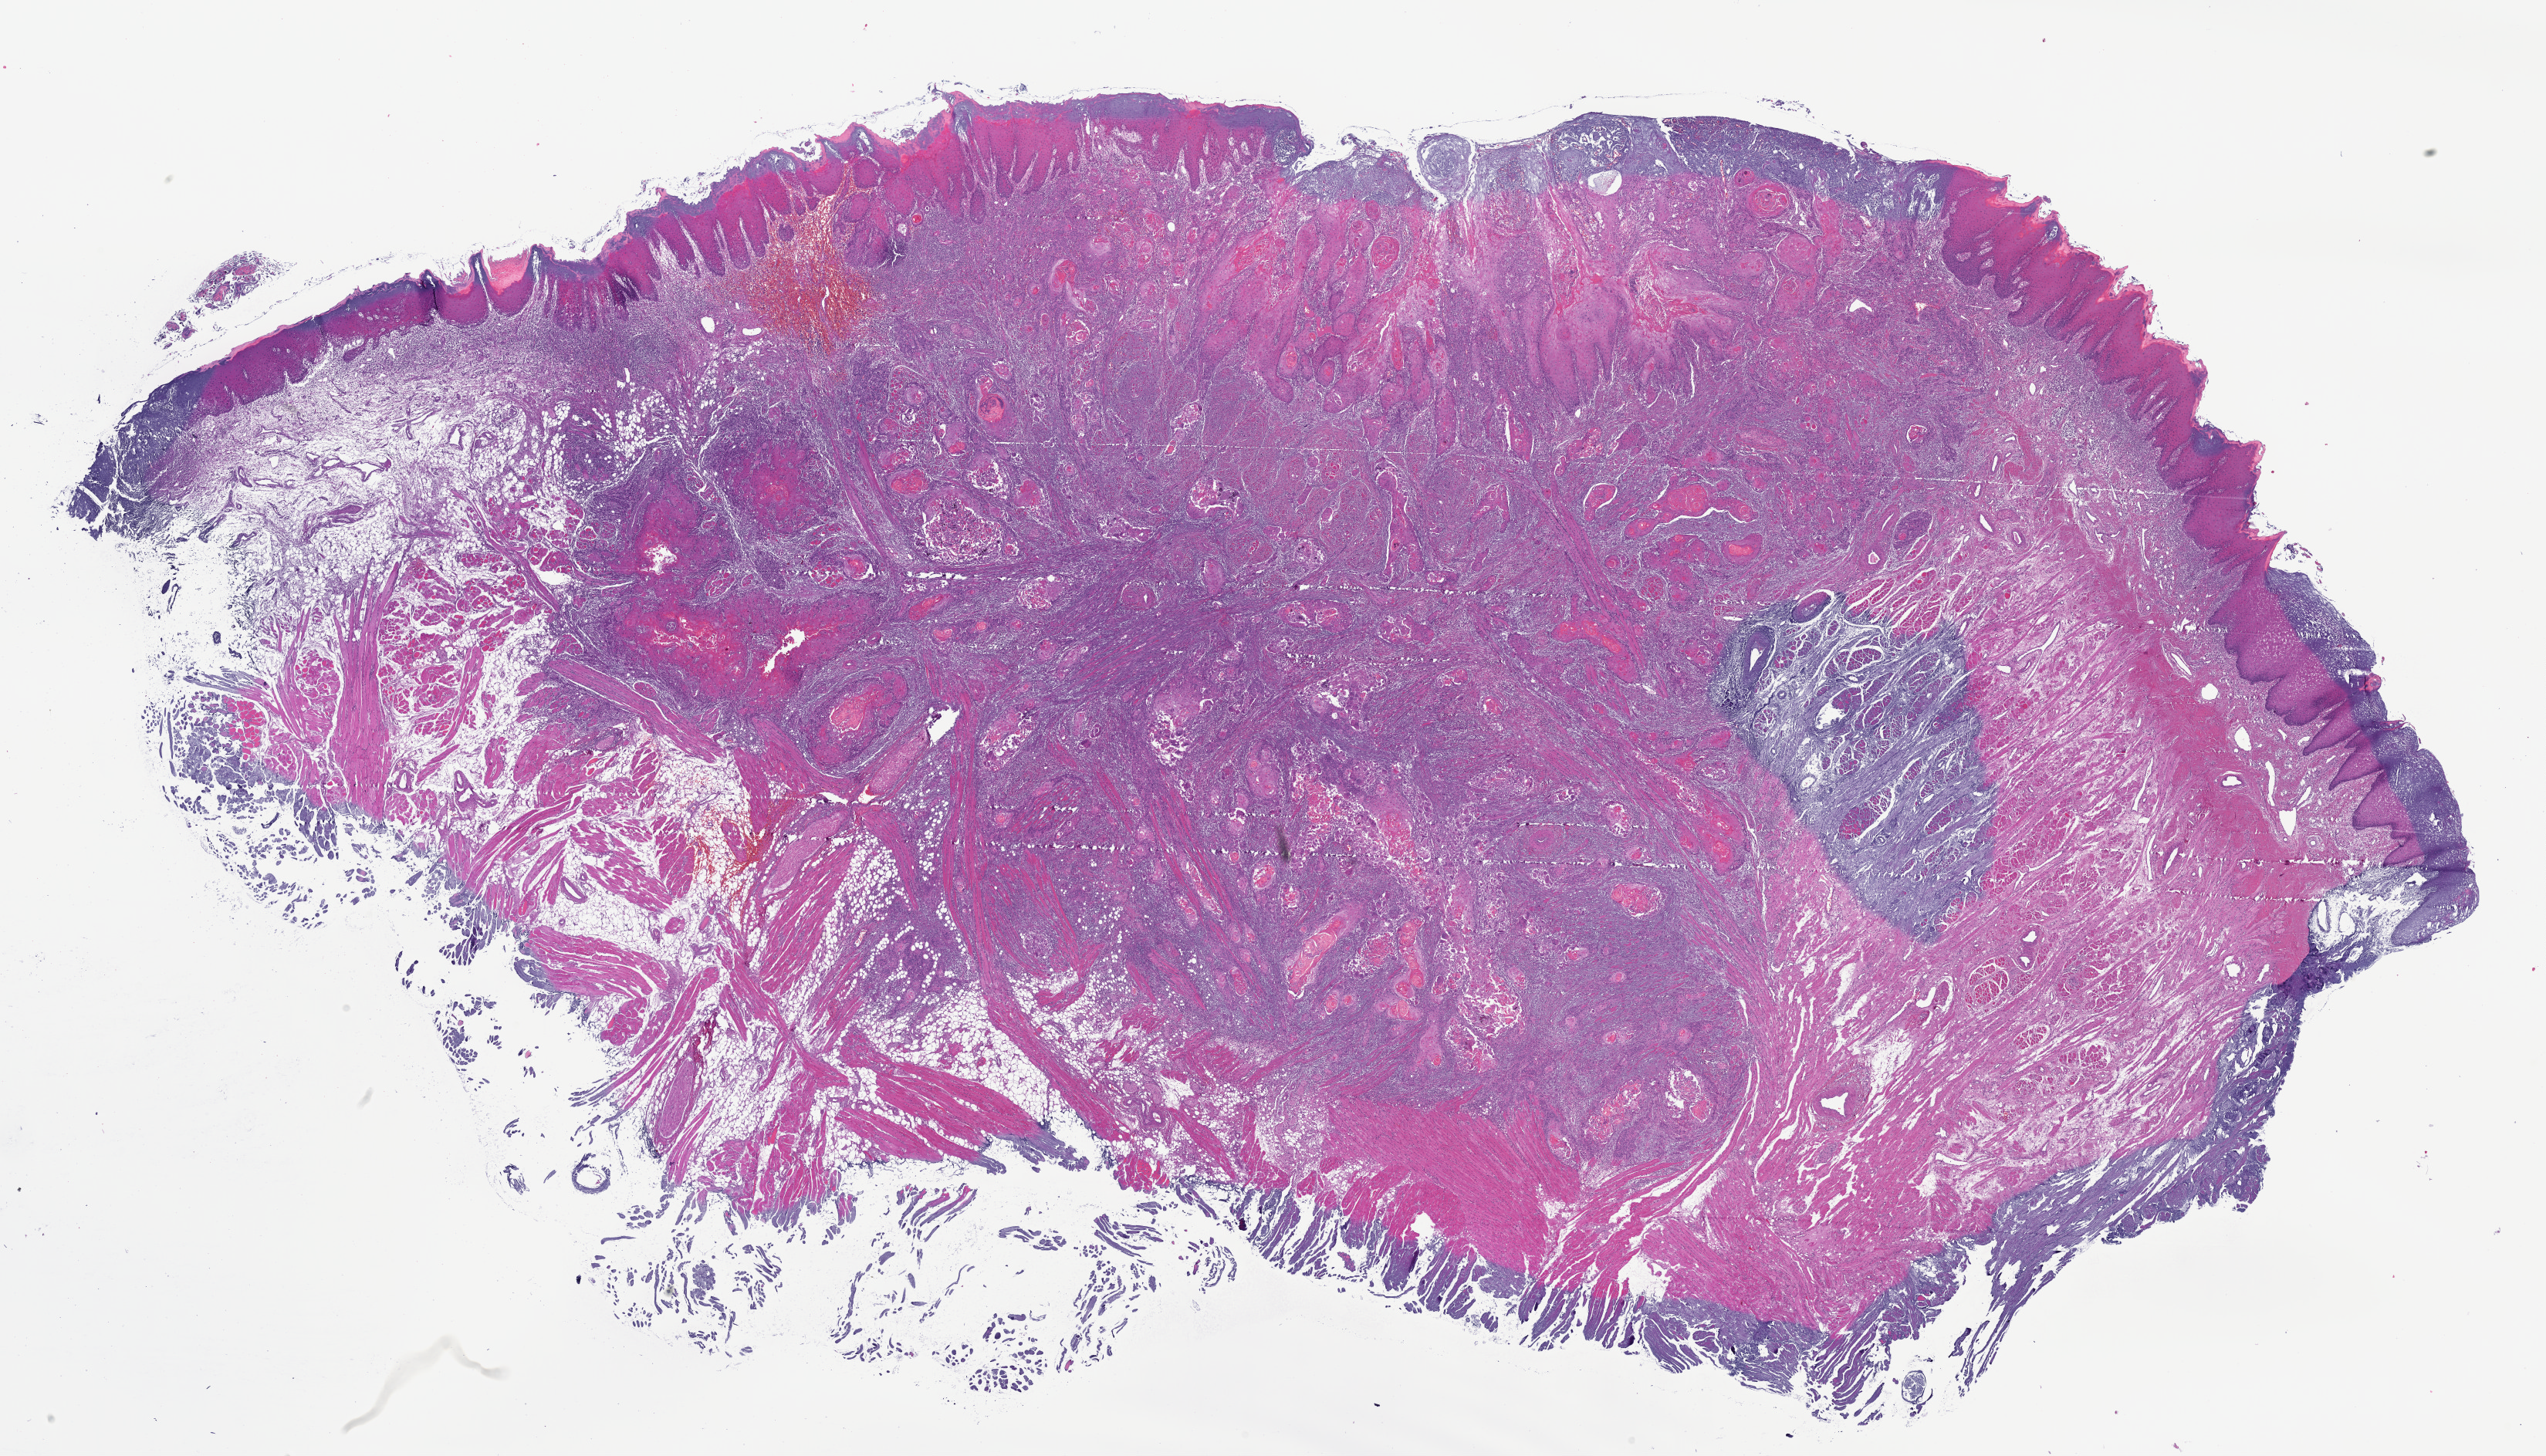
H&E-stained whole-slide image, a low-resolution overview of the entire scanned area, about 26.7 x 15.2 mm, formalin-fixed paraffin-embedded (FFPE) diagnostic section, primary tumour sample from the head and neck. Male, age 46 years at initial diagnosis. Histologic grade: G1 (well differentiated).
AJCC pathologic stage: III. Histologic diagnosis: Squamous cell carcinoma, keratinizing, NOS (tongue, NOS). Lymph nodes positive (case pathology): 1 of 26 examined.